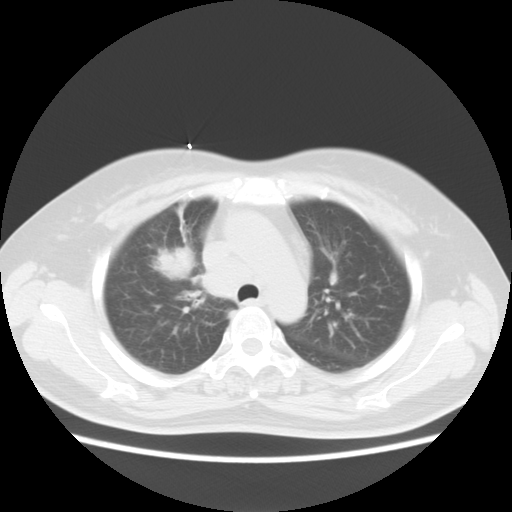
Chest CT, one axial slice. Slice 11 of 18 in the series (ordered by position). Lung window (W 1500 / L -600 HU). 5 mm slice thickness. 512 × 512 image matrix, field of view 350 × 350 mm. Female patient, age 54 years. Case-level facts recorded for this patient, not image findings: clinical TNM (as recorded): T2 N3 M0; histopathological grade: G3.
Annotated regions visible in this slice (bounding box drawn by a radiologist):
- lung tumour (recorded histology: small cell carcinoma): bounding box [x1, y1, x2, y2] px = [156, 244, 196, 282]